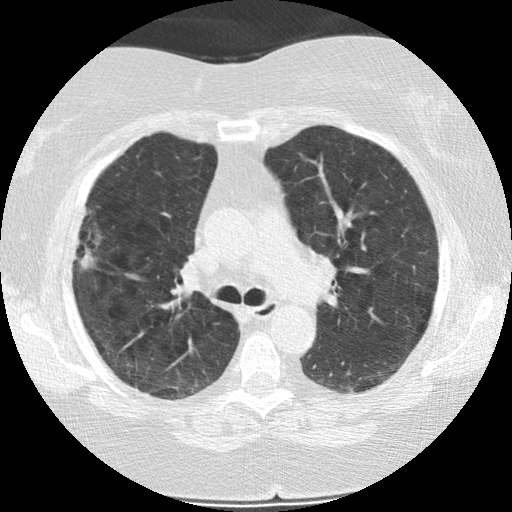
Low-dose screening chest CT, axial slice, first (baseline) screen, lung window (W 1500 / L -600 HU), 2.5 mm slice thickness, 512 × 512 image matrix. Female, age 73 years at enrolment.
• Expert-annotated lung lesion, box from (x=60, y=209) to (x=109, y=275) px.
• Reader record for this screening exam (exam-level; its link to the box is not recorded): non-calcified nodule or mass ≥4 mm, right upper lobe, 21 × 14 mm, poorly defined margins, soft tissue attenuation.
• Official screen result: positive, change unspecified: nodule(s) >= 4 mm or enlarging nodule(s), mass(es), or other non-specific abnormalities suspicious for lung cancer.
• Participant outcome: lung cancer diagnosed 482 days after this screen (after the second annual screen) — bronchiolo-alveolar adenocarcinoma, NOS, right upper lobe, moderately differentiated (G2), stage IIIB (AJCC 6th edition), 21 mm at pathology.